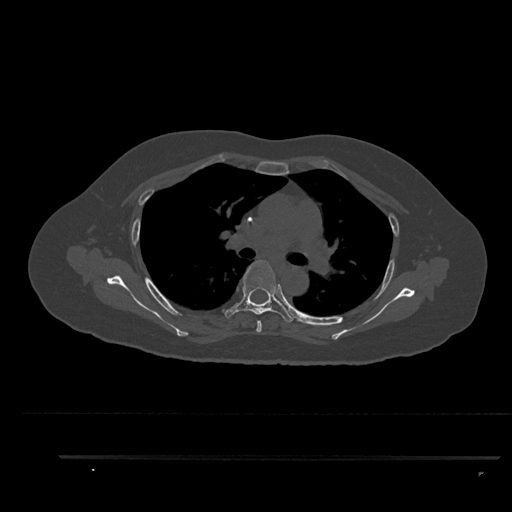
CT including the spine, one axial slice. Slice 610 of 797 in the series (ordered by position). Reconstruction kernel Br40s/3. 120 kVp. Bone window (W 1800 / L 400 HU). 0.5 mm slice thickness. 512 × 512 image matrix, field of view 408 × 408 mm. Female patient, age 44 years. From the clinical record (not read from this slice): primary cancer: renal; vertebrae with lytic lesions (as recorded): L1.
Annotated regions visible in this slice (semi-automatic segmentation, software-assisted and operator-edited):
- T4 vertebra: box from (x=256, y=320) to (x=262, y=333) px
- T5 vertebra: (x=222, y=260)–(x=294, y=322)